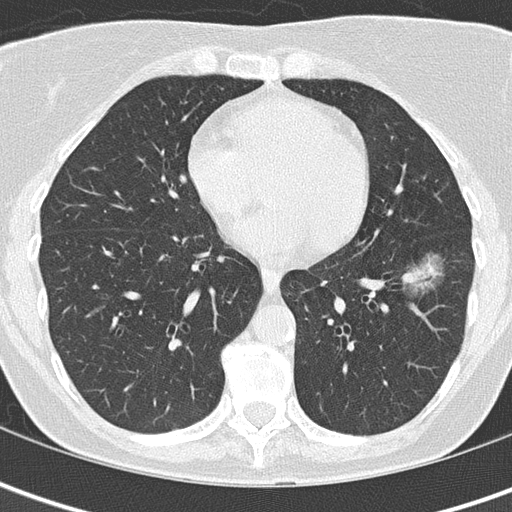
Low-dose screening chest CT, one axial slice. Slice 61 of 149 in the series (ordered by position). Lung window (W 1500 / L -600 HU). 2 mm slice thickness. 512 × 512 image matrix, field of view 280 × 280 mm.
Structures marked on this image (manually delineated by an expert):
- lesion 1 (tumor, lower lobe of left lung): bounding box (x1, y1, x2, y2) in pixels: (405, 259, 438, 288)